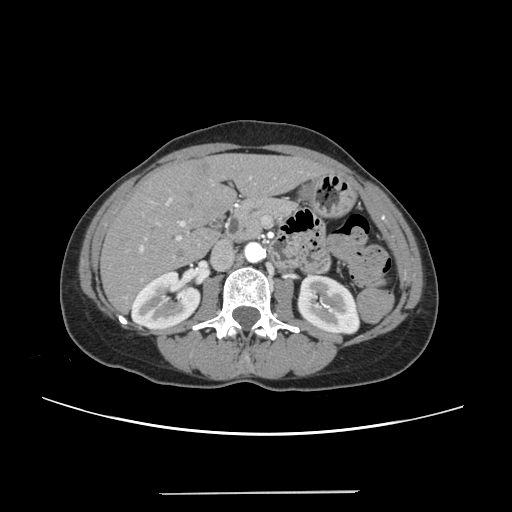
Contrast-enhanced abdominal CT, one axial slice; slice 113 of 240 in the series (ordered by position); intravenous contrast given; soft-tissue window (W 400 / L 40 HU); 1.25 mm slice thickness; 512 × 512 image matrix, field of view 371 × 371 mm. Female patient, age 60 years. From the clinical record (not read from this slice): diagnosis: colorectal cancer liver metastases, imaged before liver resection; multiple liver metastases: no.
Annotated regions visible in this slice (expert manual segmentation):
- liver: bounding box (x1, y1, x2, y2) in pixels: (102, 155, 325, 311)
- planned liver remnant (the part of the liver to remain after resection): (102, 156, 325, 310)
- portal vein (with intrahepatic branches): (138, 177, 252, 280)
- liver metastasis: (199, 164, 210, 170)